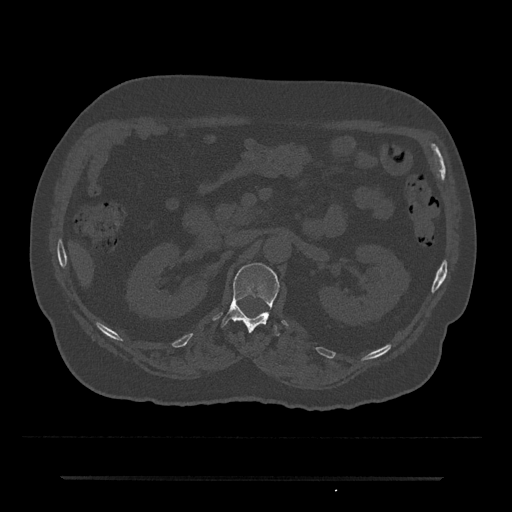
CT including the spine, one axial slice. Position 72 of 797 along the scan axis. Bone window (W 1800 / L 400 HU). 0.5 mm slice thickness. 512 × 512 image matrix. Male patient, age 69 years. Case-level facts recorded for this patient, not image findings: primary cancer: prostate.
Annotated regions visible in this slice (semi-automatically segmented with operator editing):
- L1 vertebra: box from (x=221, y=263) to (x=279, y=336) px